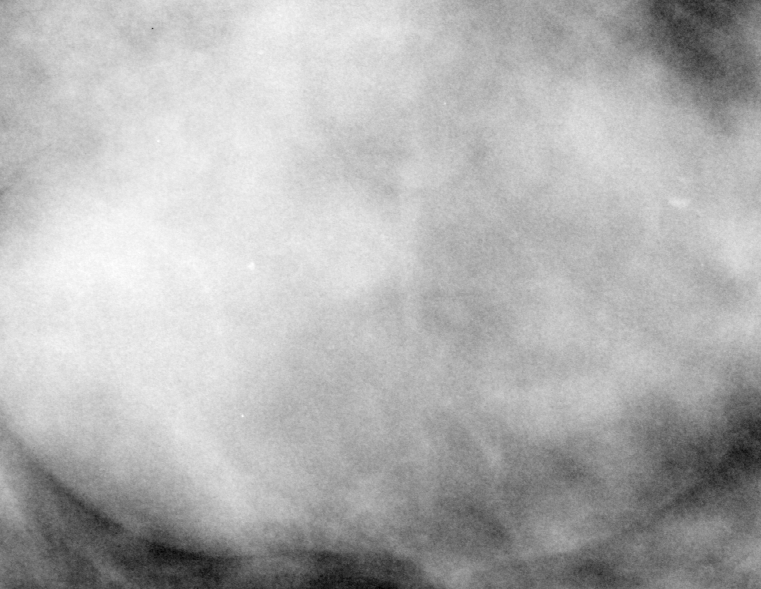
Cropped region of a digitized screen-film mammogram centred on a radiologist-marked abnormality, left breast, MLO view, BI-RADS breast density category 3 (scale 1–4).
- Mass, shape oval, margins obscured; BI-RADS assessment category 3; pathology (as recorded): benign.